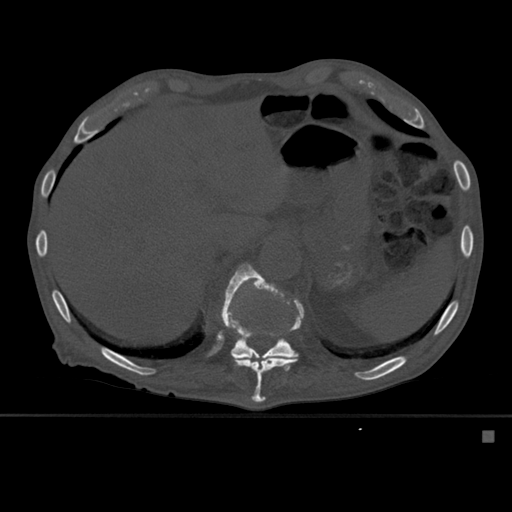
CT including the spine, one axial slice; position 286 of 527 along the scan axis; bone window (W 1800 / L 400 HU); 1.5 mm slice thickness; 512 × 512 image matrix, field of view 373 × 373 mm. Patient: male, 78 years. Case-level facts recorded for this patient, not image findings: primary cancer: prostate.
Outlined on this slice (semi-automatically segmented with operator editing):
- T11 vertebra: bounding box [x1, y1, x2, y2] px = [221, 263, 304, 403]
- T12 vertebra: [221, 276, 304, 358]